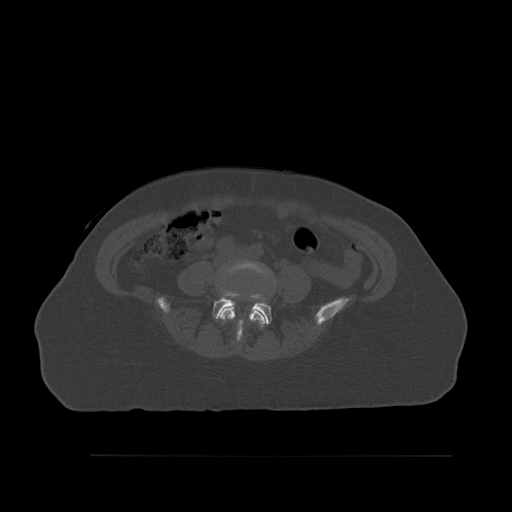
CT including the spine, one axial slice. Position 197 of 527 along the scan axis. Bone window (W 1800 / L 400 HU). 512 × 512 image matrix, field of view 470 × 470 mm. Female patient, age 73 years. Case-level facts recorded for this patient, not image findings: primary cancer: breast; vertebrae with lytic lesions (as recorded): L2.
Annotated regions visible in this slice (semi-automatically segmented with operator editing):
- L4 vertebra: bounding box [x1, y1, x2, y2] px = [220, 261, 271, 342]
- L5 vertebra: [212, 292, 272, 325]